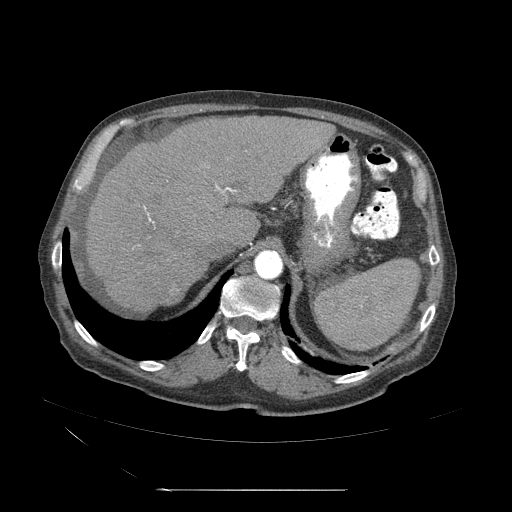
Contrast-enhanced abdominal CT (liver protocol), one axial slice. Position 36 of 71 along the scan axis. Reconstruction kernel STANDARD. 120 kVp. Soft-tissue window (W 400 / L 40 HU). 2.5 mm slice thickness. 512 × 512 image matrix, field of view 440 × 440 mm. From the clinical record (not read from this slice): diagnosis: hepatocellular carcinoma (patient treated with transarterial chemoembolisation; whether this scan precedes or follows treatment is not stated here); TNM stage (as recorded): Stage-II; Child-Pugh class: A; tumour nodularity: multinodular.
Structures marked on this image (semi-automatically segmented with operator editing):
- abdominal aorta: box from (x=253, y=250) to (x=283, y=279) px
- liver parenchyma outside the tumour (the mass and vessels are separate outlines, so this box may not span the whole liver): (x=79, y=117)–(x=335, y=321)
- mass: (x=159, y=285)–(x=180, y=305)
- liver vessels: (x=134, y=161)–(x=235, y=290)